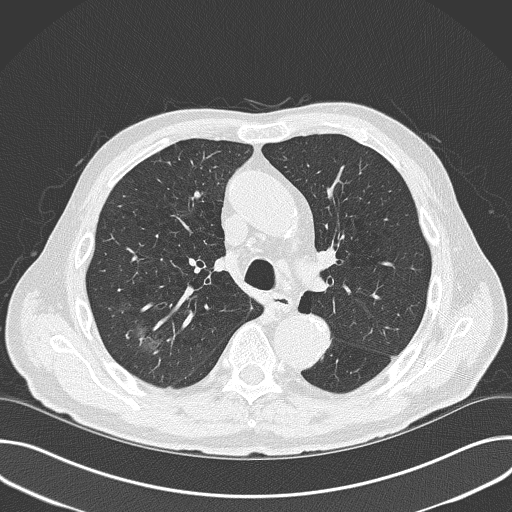
Low-dose screening chest CT, one axial slice; reconstruction kernel B50f; 120 kVp; lung window (W 1500 / L -600 HU); 2 mm slice thickness; 512 × 512 image matrix, field of view 380 × 380 mm.
Structures marked on this image (outlined manually by an expert reader):
- lesion 1 (tumor, upper lobe of right lung): box from (x=137, y=325) to (x=163, y=348) px